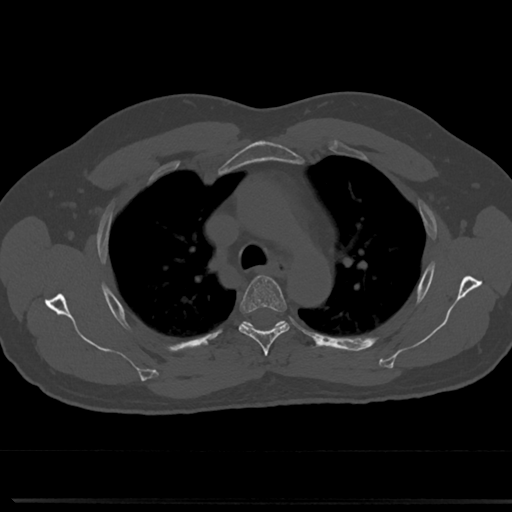
CT including the spine, one axial slice; slice 537 of 817 in the series (ordered by position); reconstruction kernel Br40s/3; 120 kVp; bone window (W 1800 / L 400 HU); 0.5 mm slice thickness; 512 × 512 image matrix. Male patient, age 61 years. Case-level facts recorded for this patient, not image findings: primary cancer: prostate.
Outlined on this slice (semi-automatic segmentation, software-assisted and operator-edited):
- T4 vertebra: bounding box (x1, y1, x2, y2) in pixels: (237, 275, 290, 354)
- T5 vertebra: (246, 322, 283, 326)